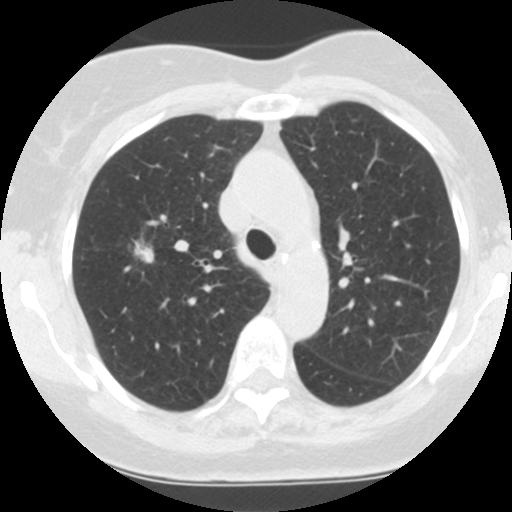
Chest CT (low-dose screening protocol), one axial image, third annual screen, lung window (W 1500 / L -600 HU), 2.5 mm slice thickness, standard (soft-tissue) reconstruction kernel (STANDARD), slice 152 of 212 in the series. Female, age 62 years at enrolment. Former smoker at enrolment.
Expert-annotated lung lesion, bounding box [x1, y1, x2, y2] px = [116, 227, 175, 282]. The exam's reader record, not a measurement of the box and not confirmed to be the same lesion: non-calcified nodule or mass ≥4 mm, right upper lobe, 14 × 9 mm, spiculated (stellate) margins, soft tissue attenuation, pre-existing on the prior screen: yes; interval growth: yes. Later outcome: lung cancer diagnosed 102 days after this screen — adenocarcinoma, NOS, right upper lobe, well differentiated (G1), stage IA (AJCC 6th edition), 7 mm at pathology.